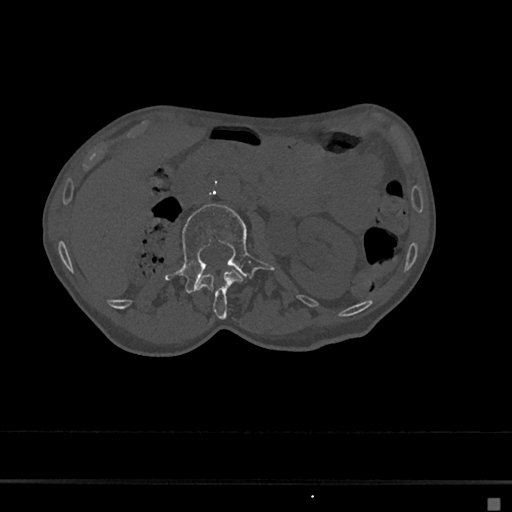
CT including the spine, one axial slice. Slice 29 of 797 in the series (ordered by position). Reconstruction kernel Br40s/3. 120 kVp. Bone window (W 1800 / L 400 HU). 512 × 512 image matrix. Patient: female, 68 years. From the clinical record (not read from this slice): primary cancer: renal.
Structures marked on this image (semi-automatic segmentation, software-assisted and operator-edited):
- L1 vertebra: box from (x=196, y=270) to (x=243, y=319) px
- L2 vertebra: (x=165, y=204)–(x=274, y=293)